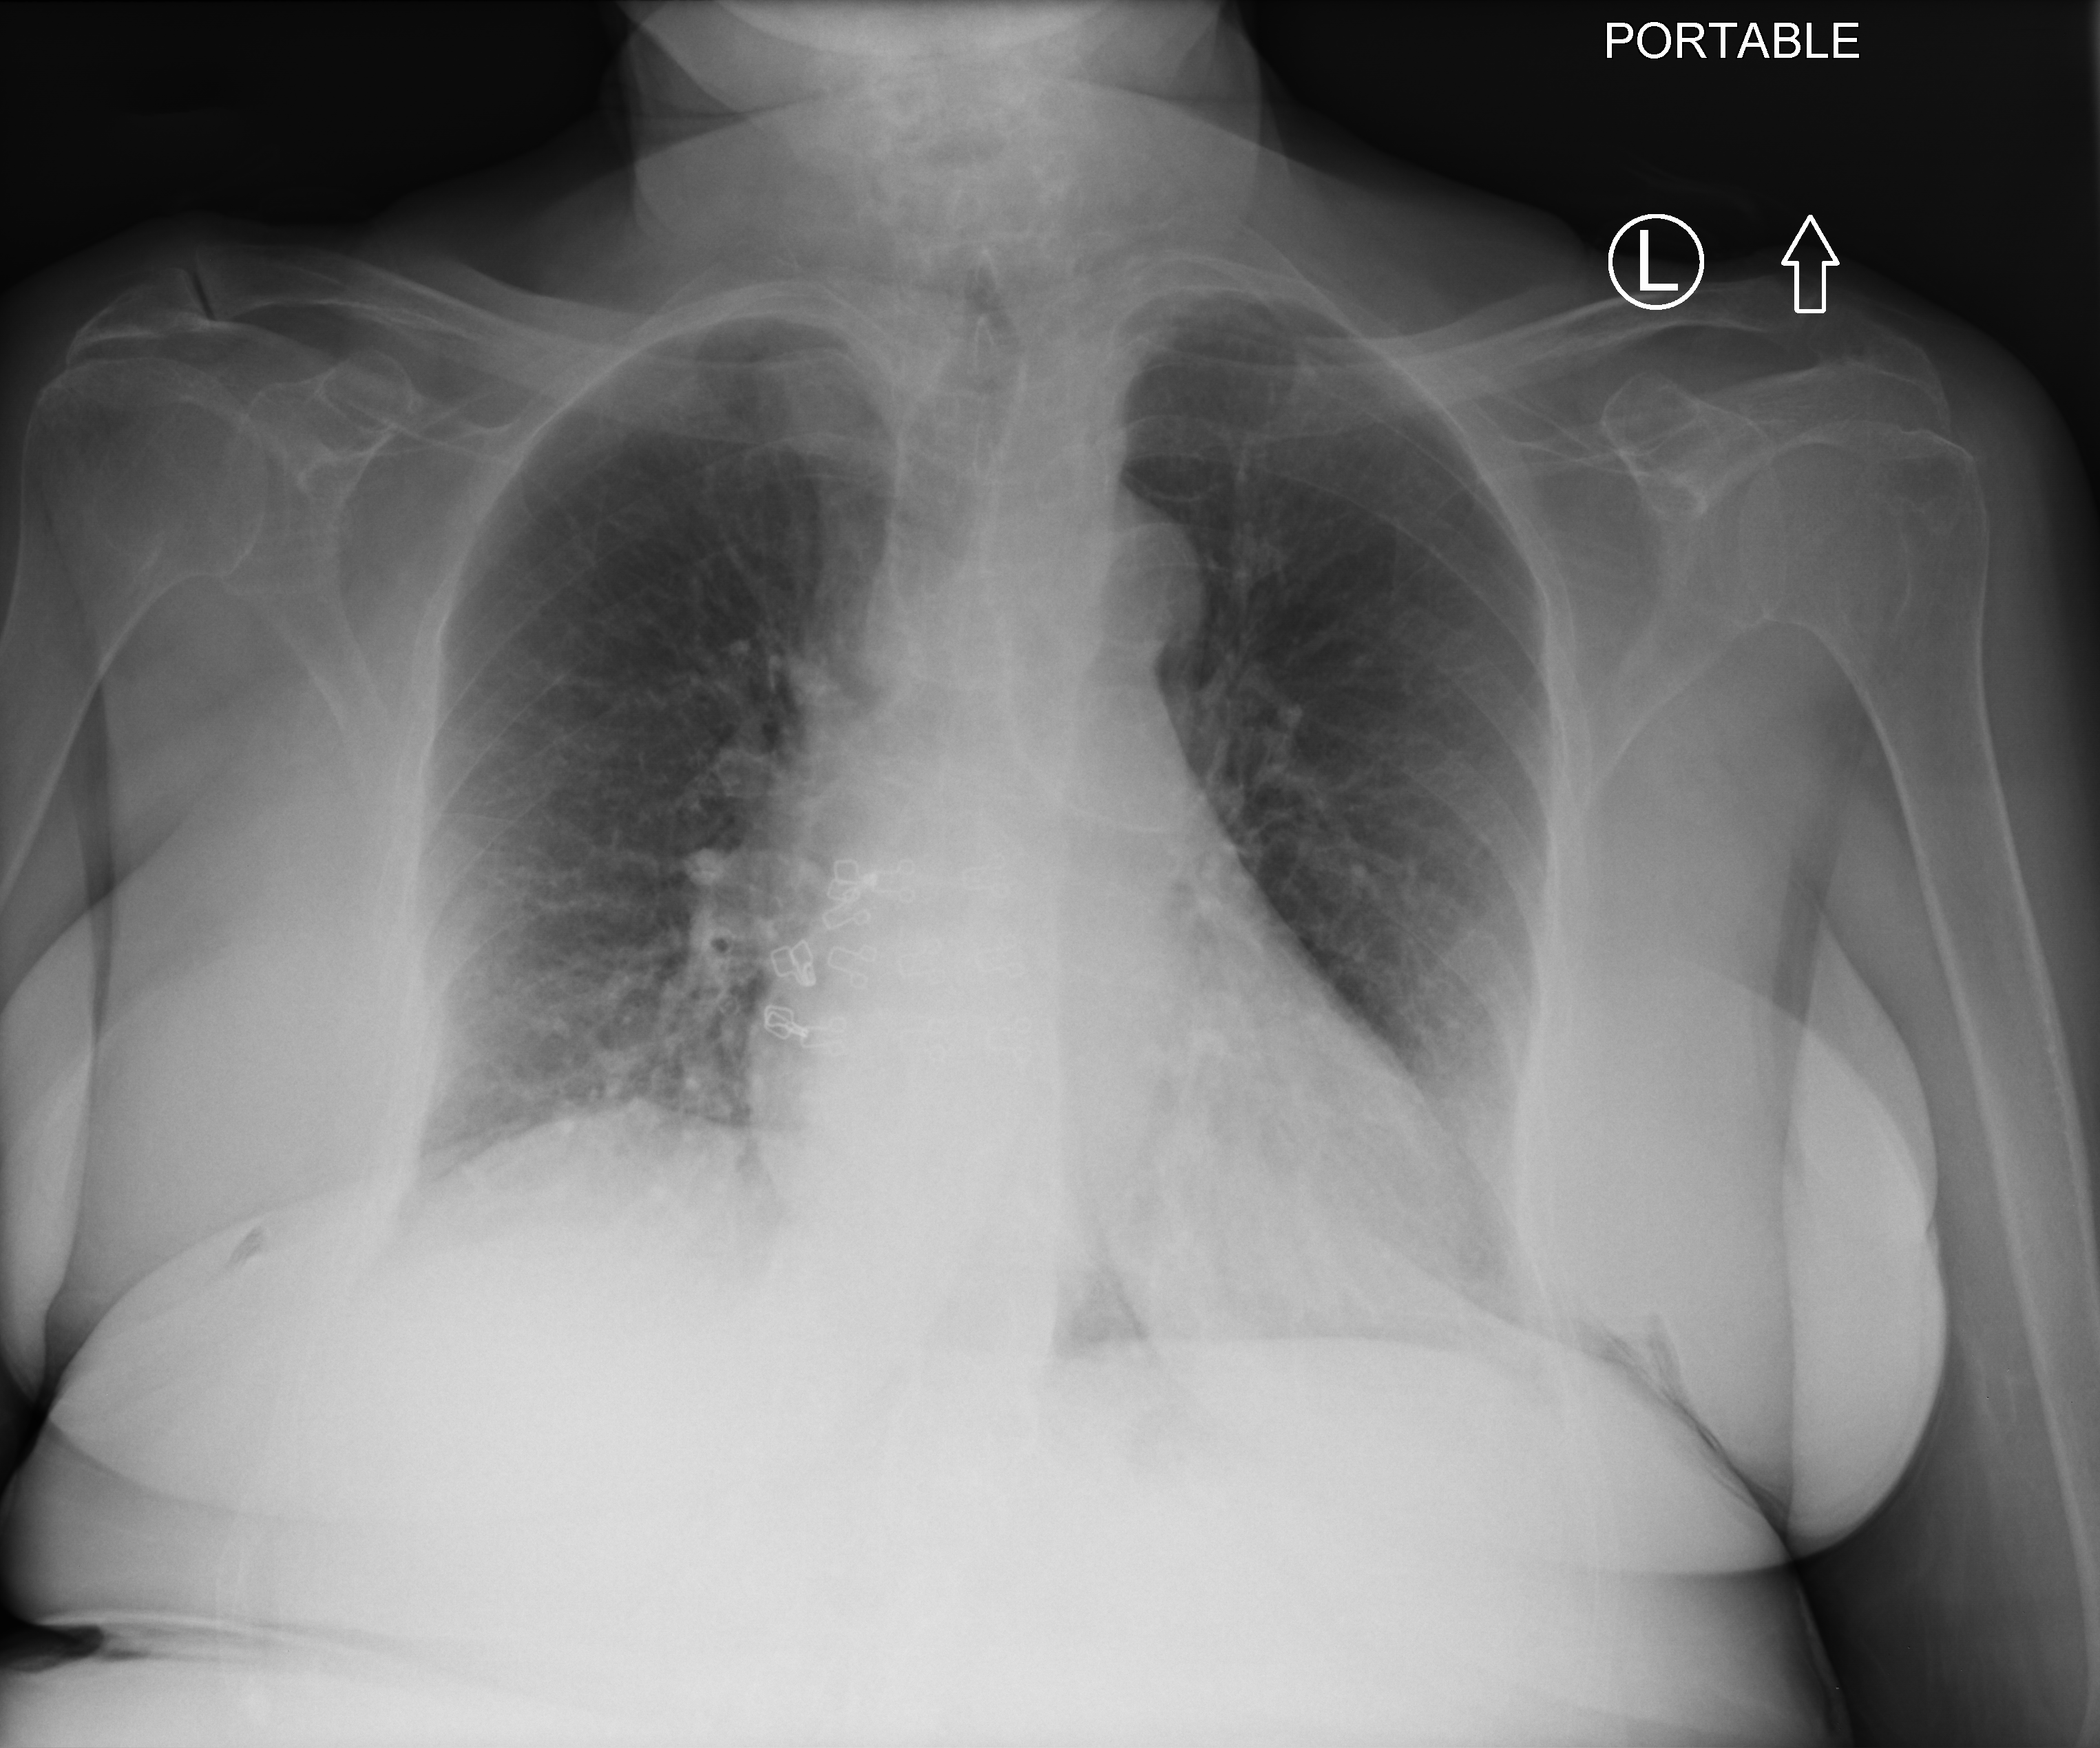
Bedside chest radiograph (computed radiography); anteroposterior (AP) projection. Patient hospitalised with COVID-19; female, aged 75–90 years.
Admission-level facts for this patient (not findings on this image; timing relative to this image not recorded): admitted to intensive care during this hospital stay: no; mechanically ventilated during this hospital stay: no.